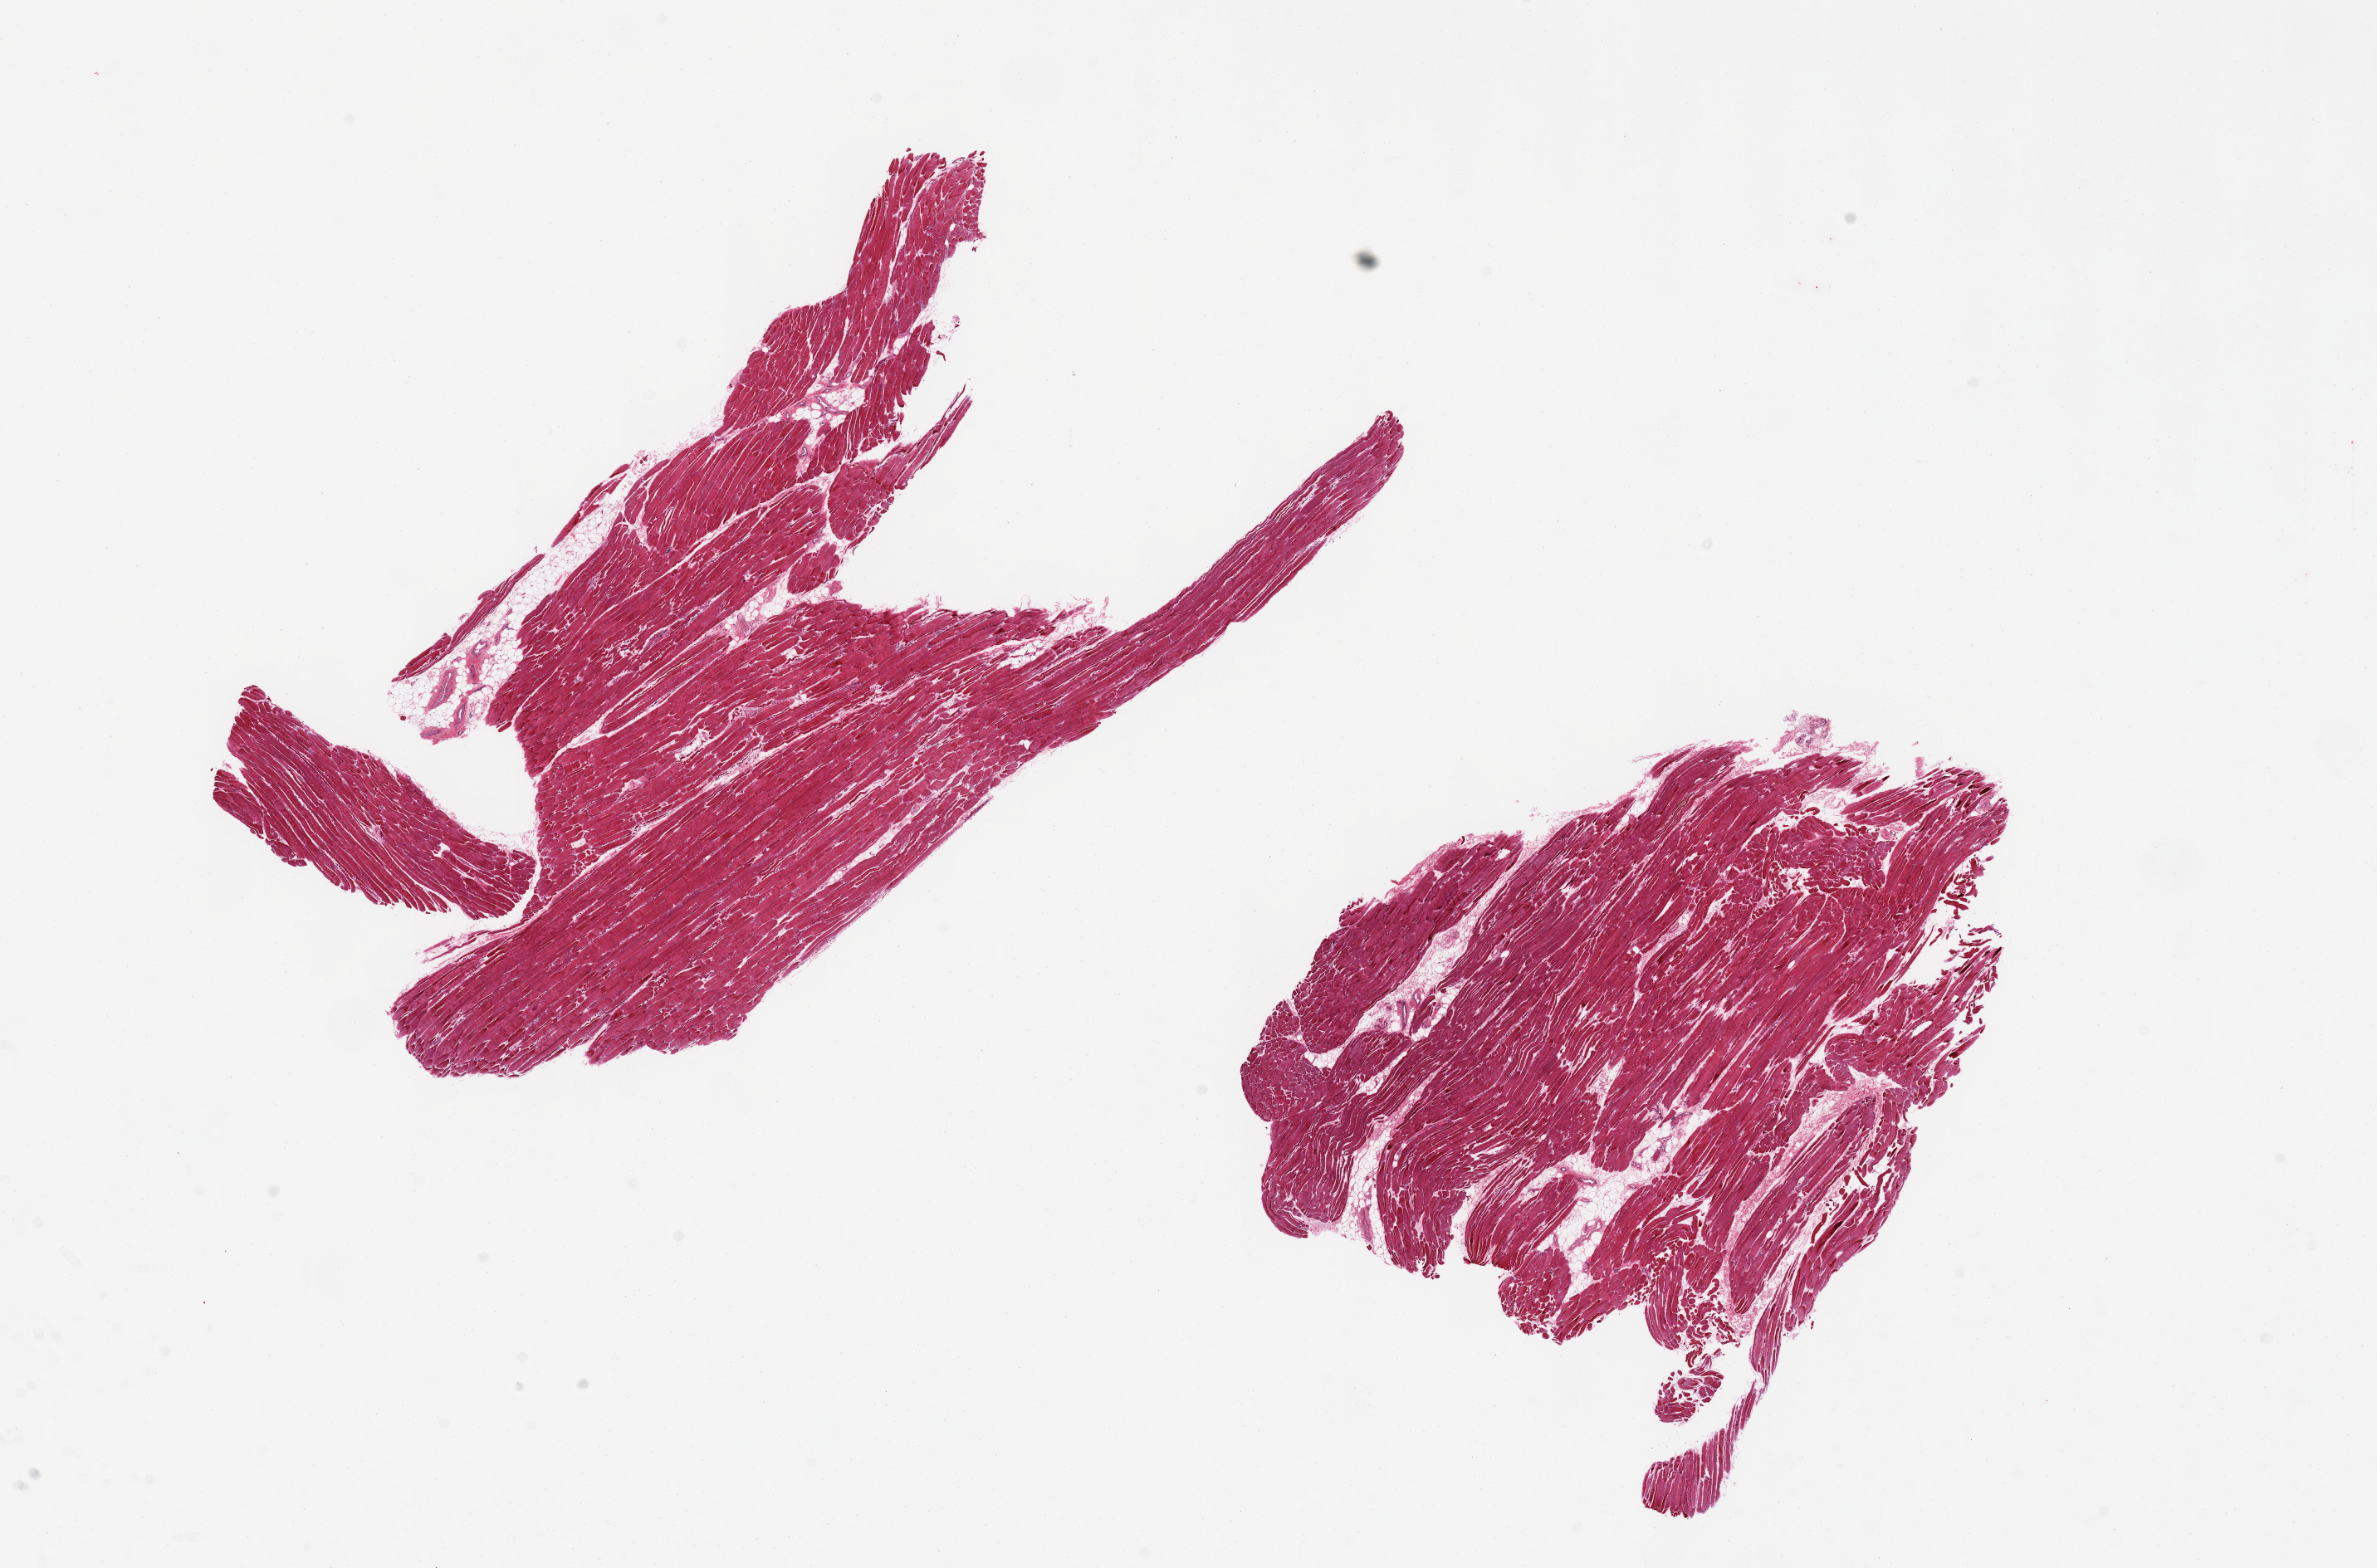
Digitized H&E-stained section — whole scanned area (about 22.6 x 14.9 mm, slide scanned at 20x) shown as a low-resolution overview, PAXgene-fixed, paraffin-embedded tissue, sampled site (target tissue): skeletal muscle, tissue donor sample. Donor sex: male.
Reviewer comment on this tissue sample: 2 pieces.